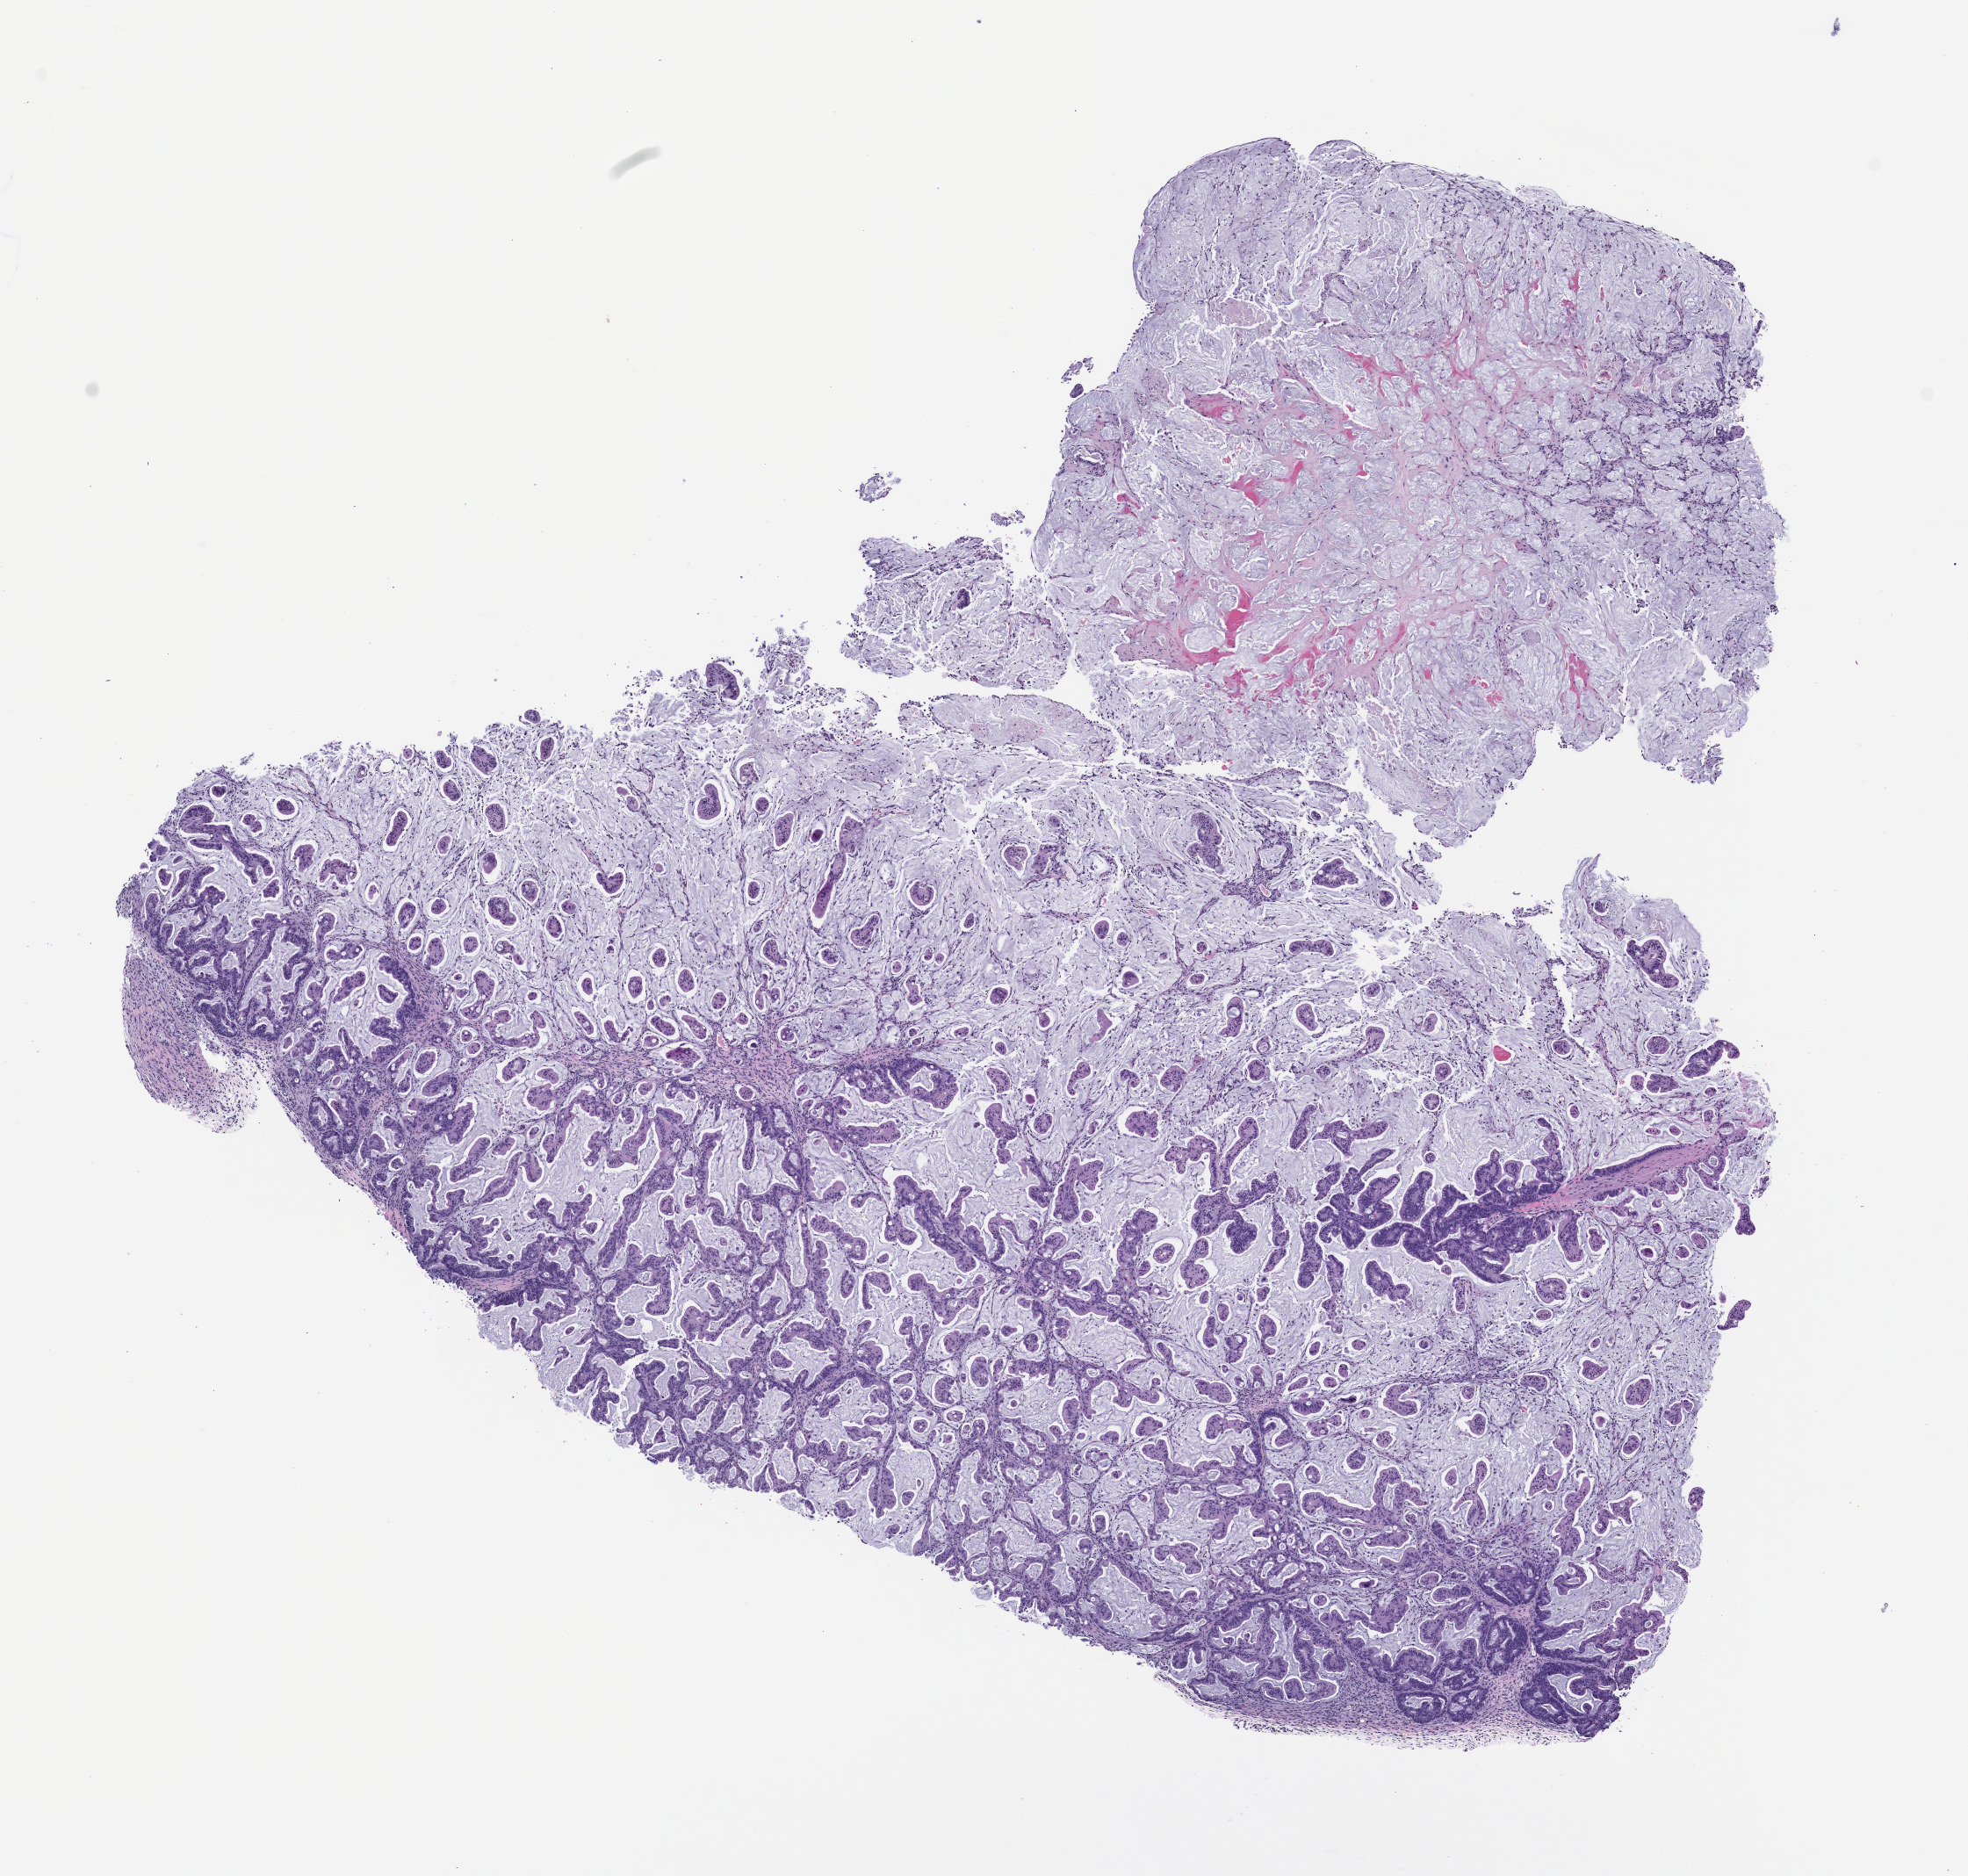
Whole-slide image, H&E: patient-derived xenograft (human tumor grown in a mouse), passage 3, low-resolution overview of the scanned area, about 9.0 x 8.6 mm; FFPE section; originating tumor site category: rectum.
Originating patient diagnosis: Rectal Adenocarcinoma.